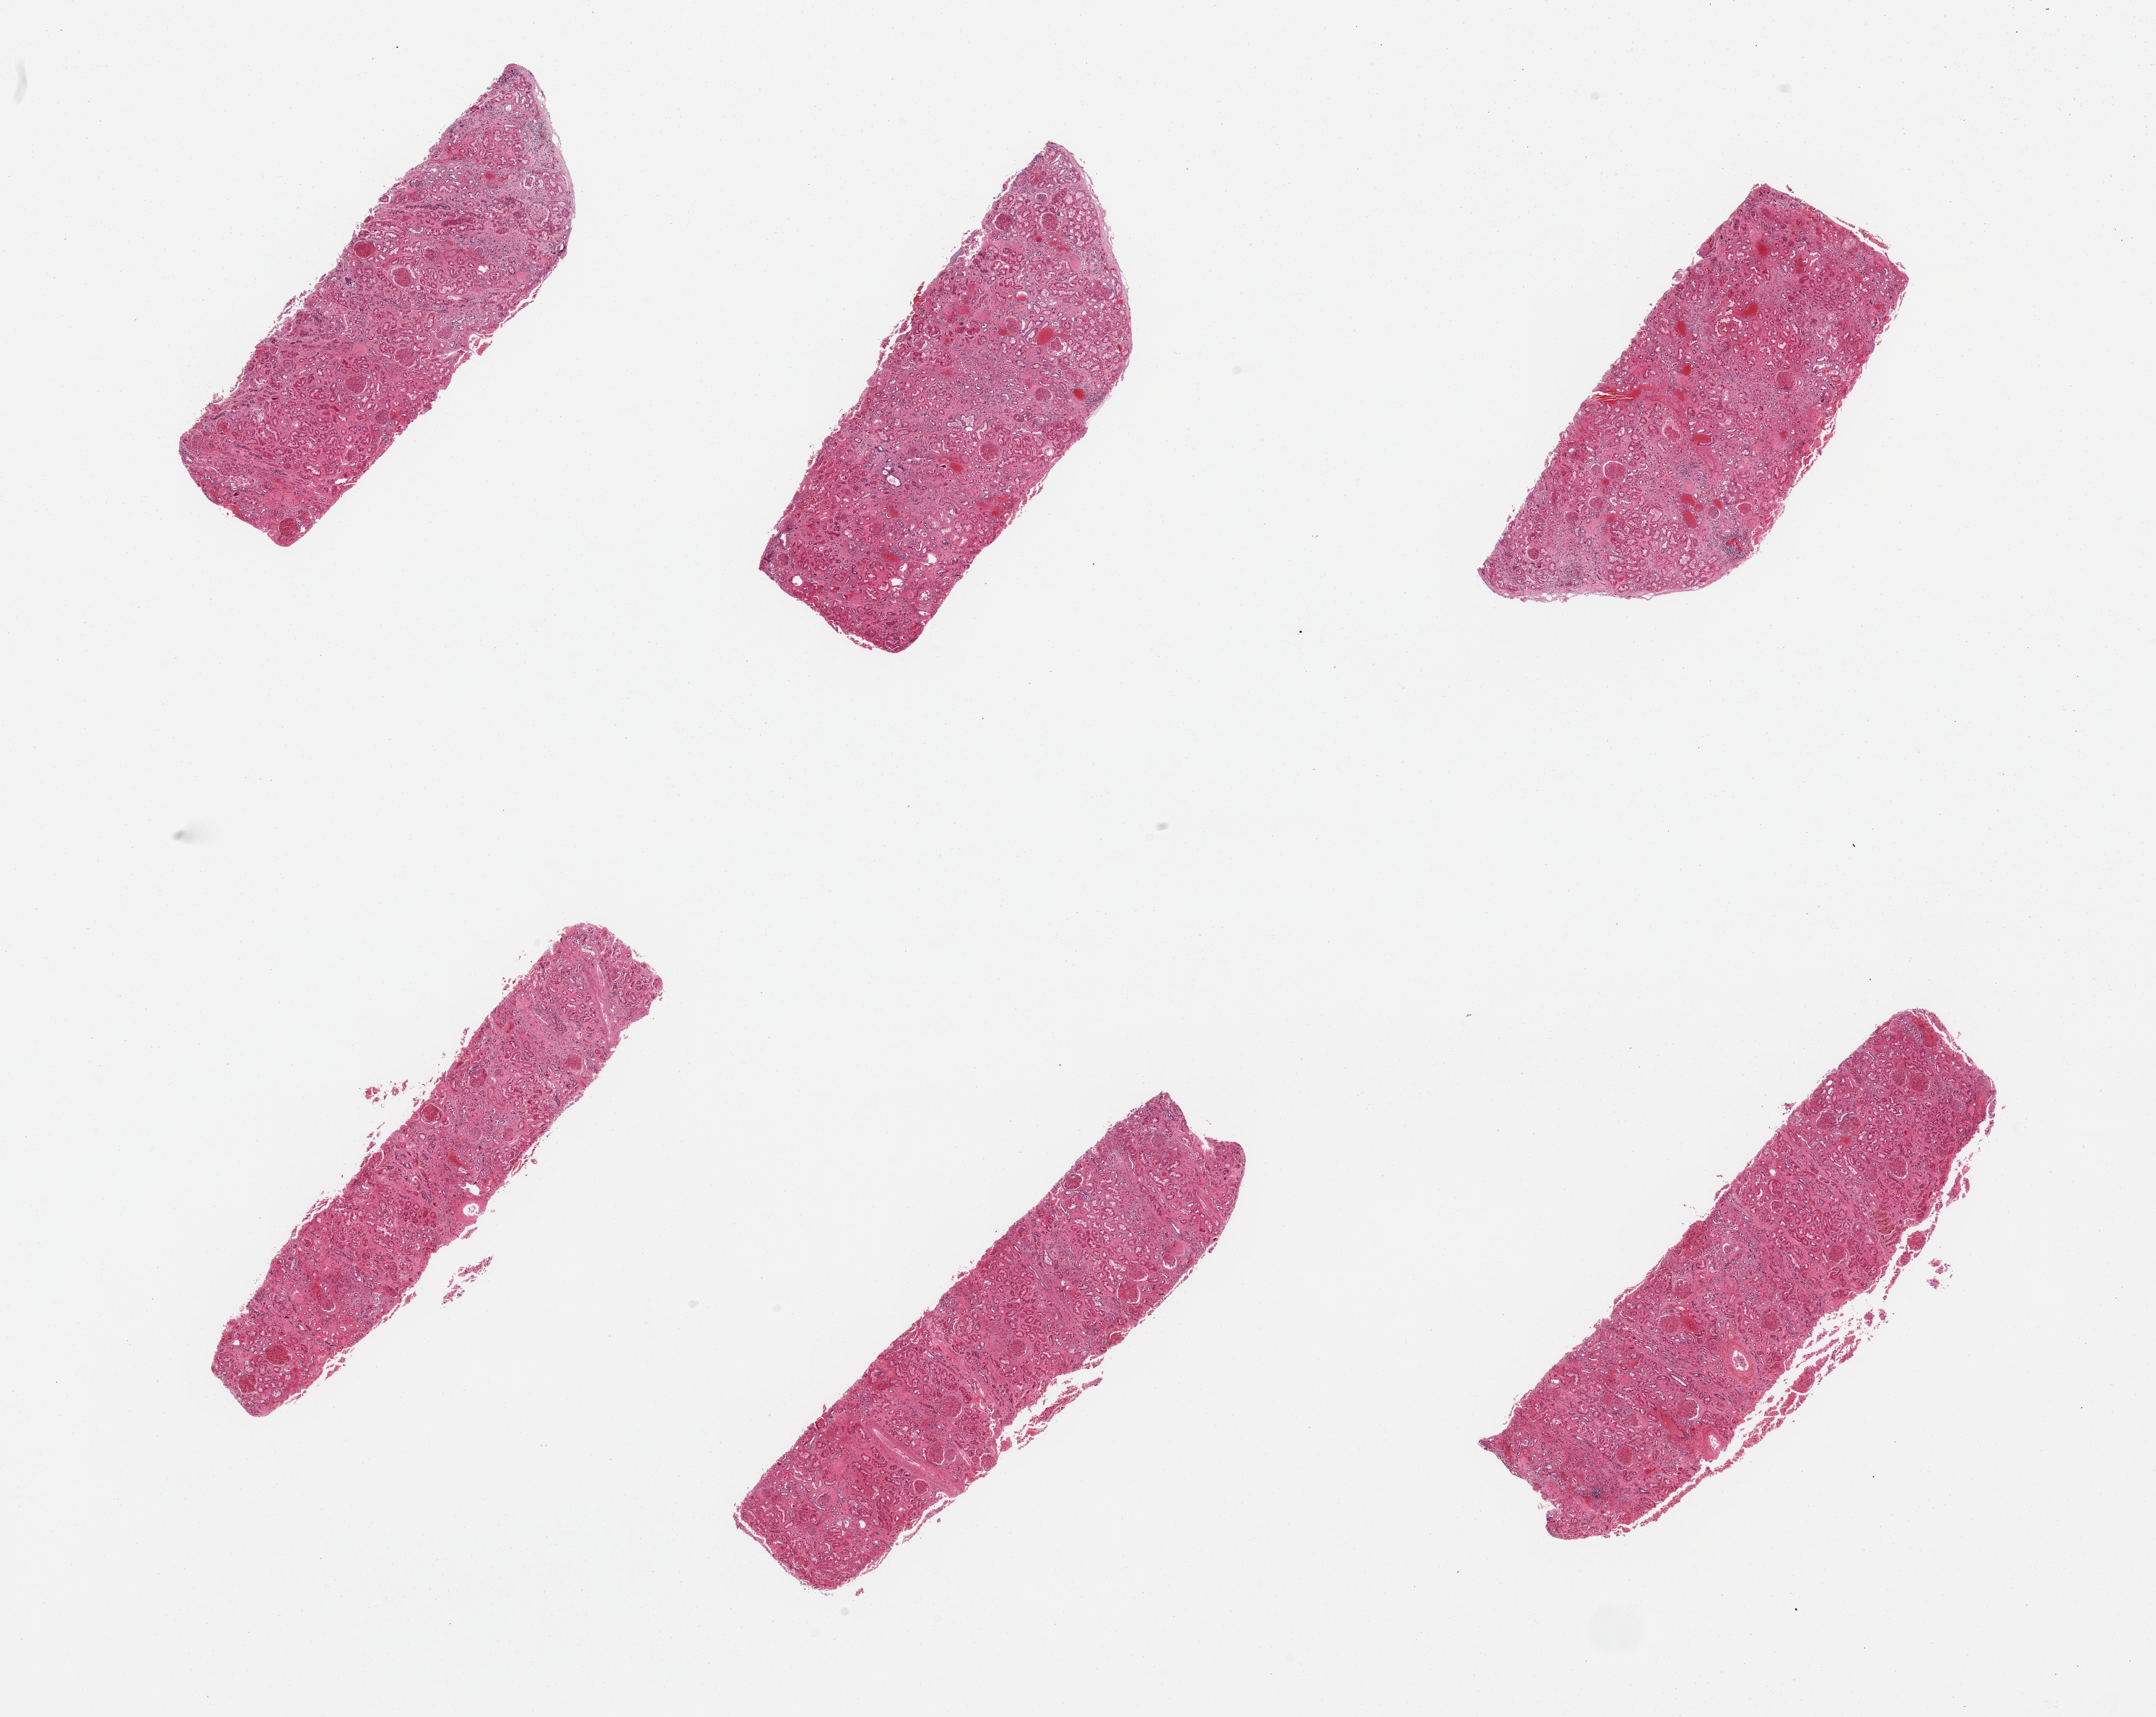
Digitized haematoxylin and eosin-stained section, whole scanned area (about 23.6 x 18.8 mm) shown as a low-resolution overview, PAXgene-fixed paraffin-embedded (PFPE) section, sampled site (target tissue): renal cortex, donor tissue sample. Male donor.
- pathologist's review note for this sample: 6 pieces, glomeruli present